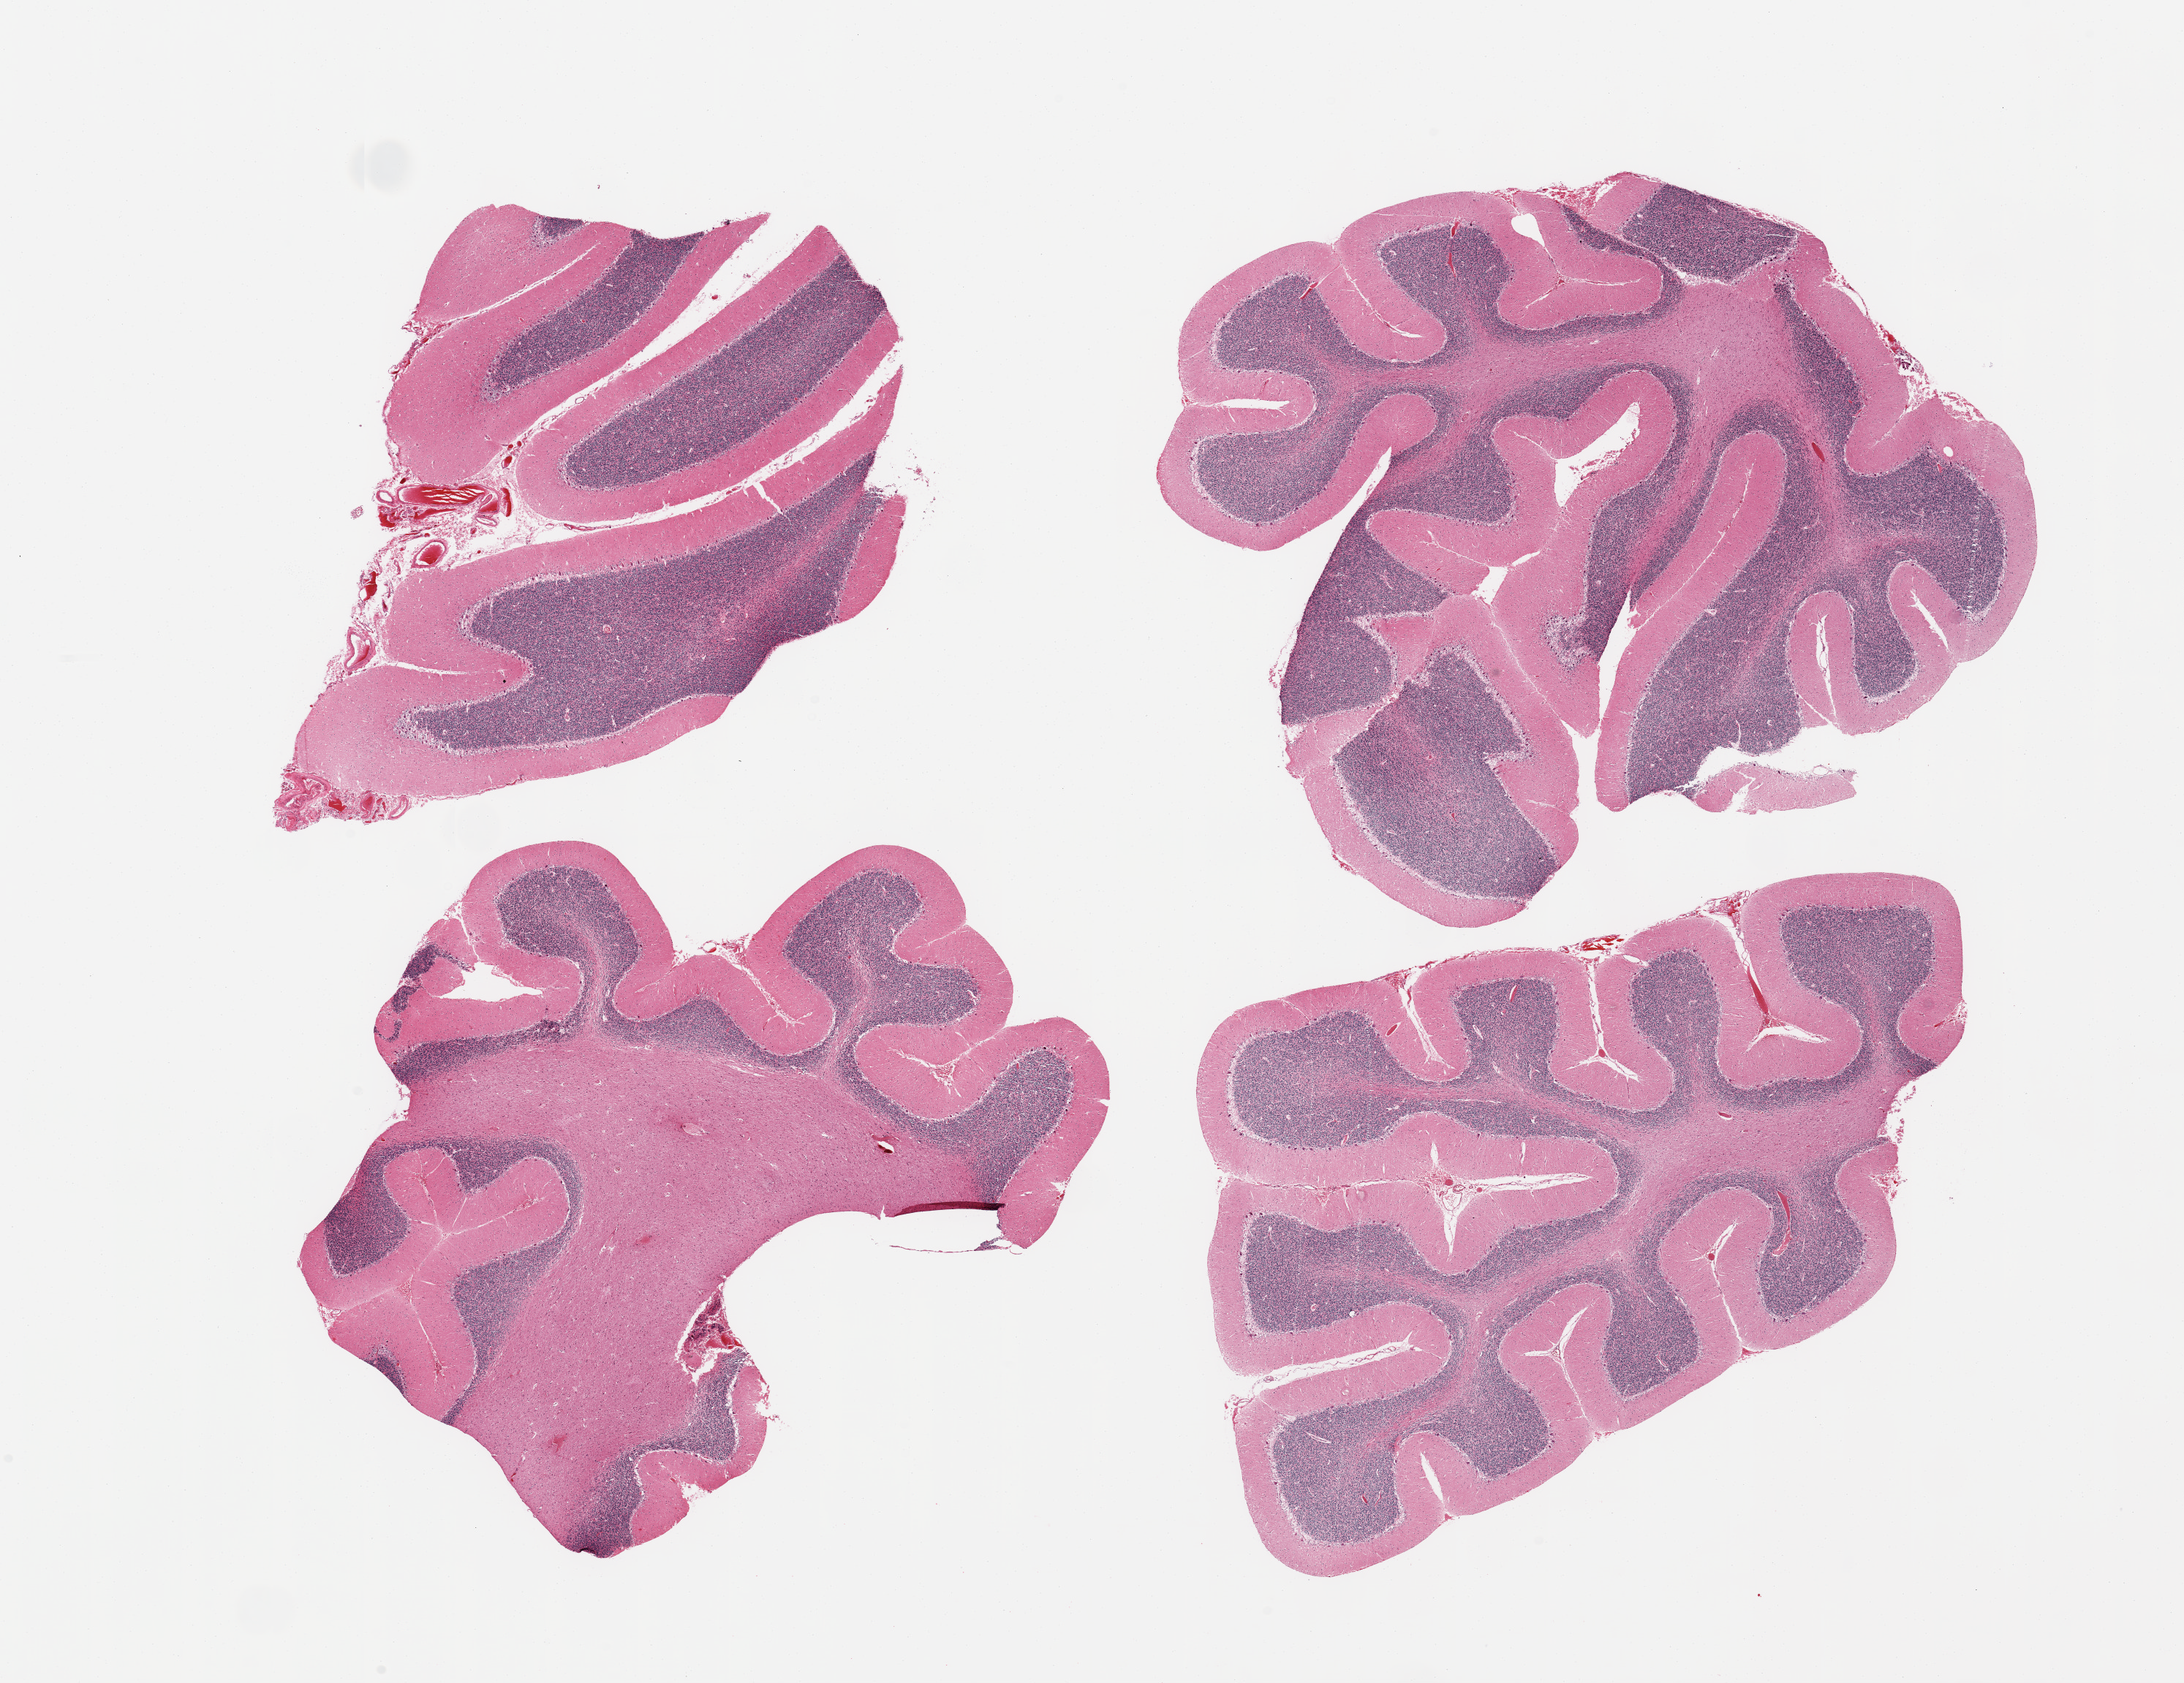
Digitized haematoxylin and eosin-stained section — low-resolution overview of the scanned area, about 23.6 x 18.2 mm (acquisition: 20x scan). PAXgene-fixed paraffin-embedded (PFPE) section. Section of cerebellum (target tissue). Tissue donor sample. Donor sex: male.
Pathologist's review note for this sample: 4 pieces, no abnormalities.